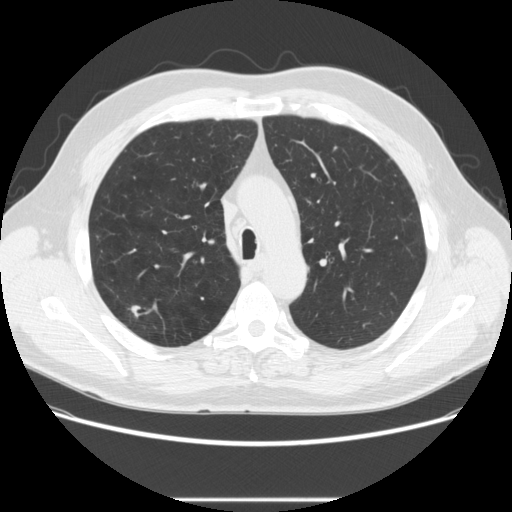
Low-dose screening chest CT, axial slice; baseline screening round; lung window (W 1500 / L -600 HU); standard (soft-tissue) reconstruction kernel (STANDARD); 120 kVp; slice 76 of 270 in the series; 512 × 512 image matrix, field of view 380 × 380 mm. Male, age 64 years at enrolment.
Expert reader's lesion annotation, bounding box [x1, y1, x2, y2] px = [118, 298, 153, 327]. The screening reader recorded 2 non-calcified nodules or masses ≥4 mm on this exam; which of them this box marks is not recorded. Later outcome: lung cancer diagnosed 753 days after this screen — adenocarcinoma, NOS, right upper lobe, moderately differentiated (G2), stage IA (AJCC 6th edition), 14 mm at pathology.